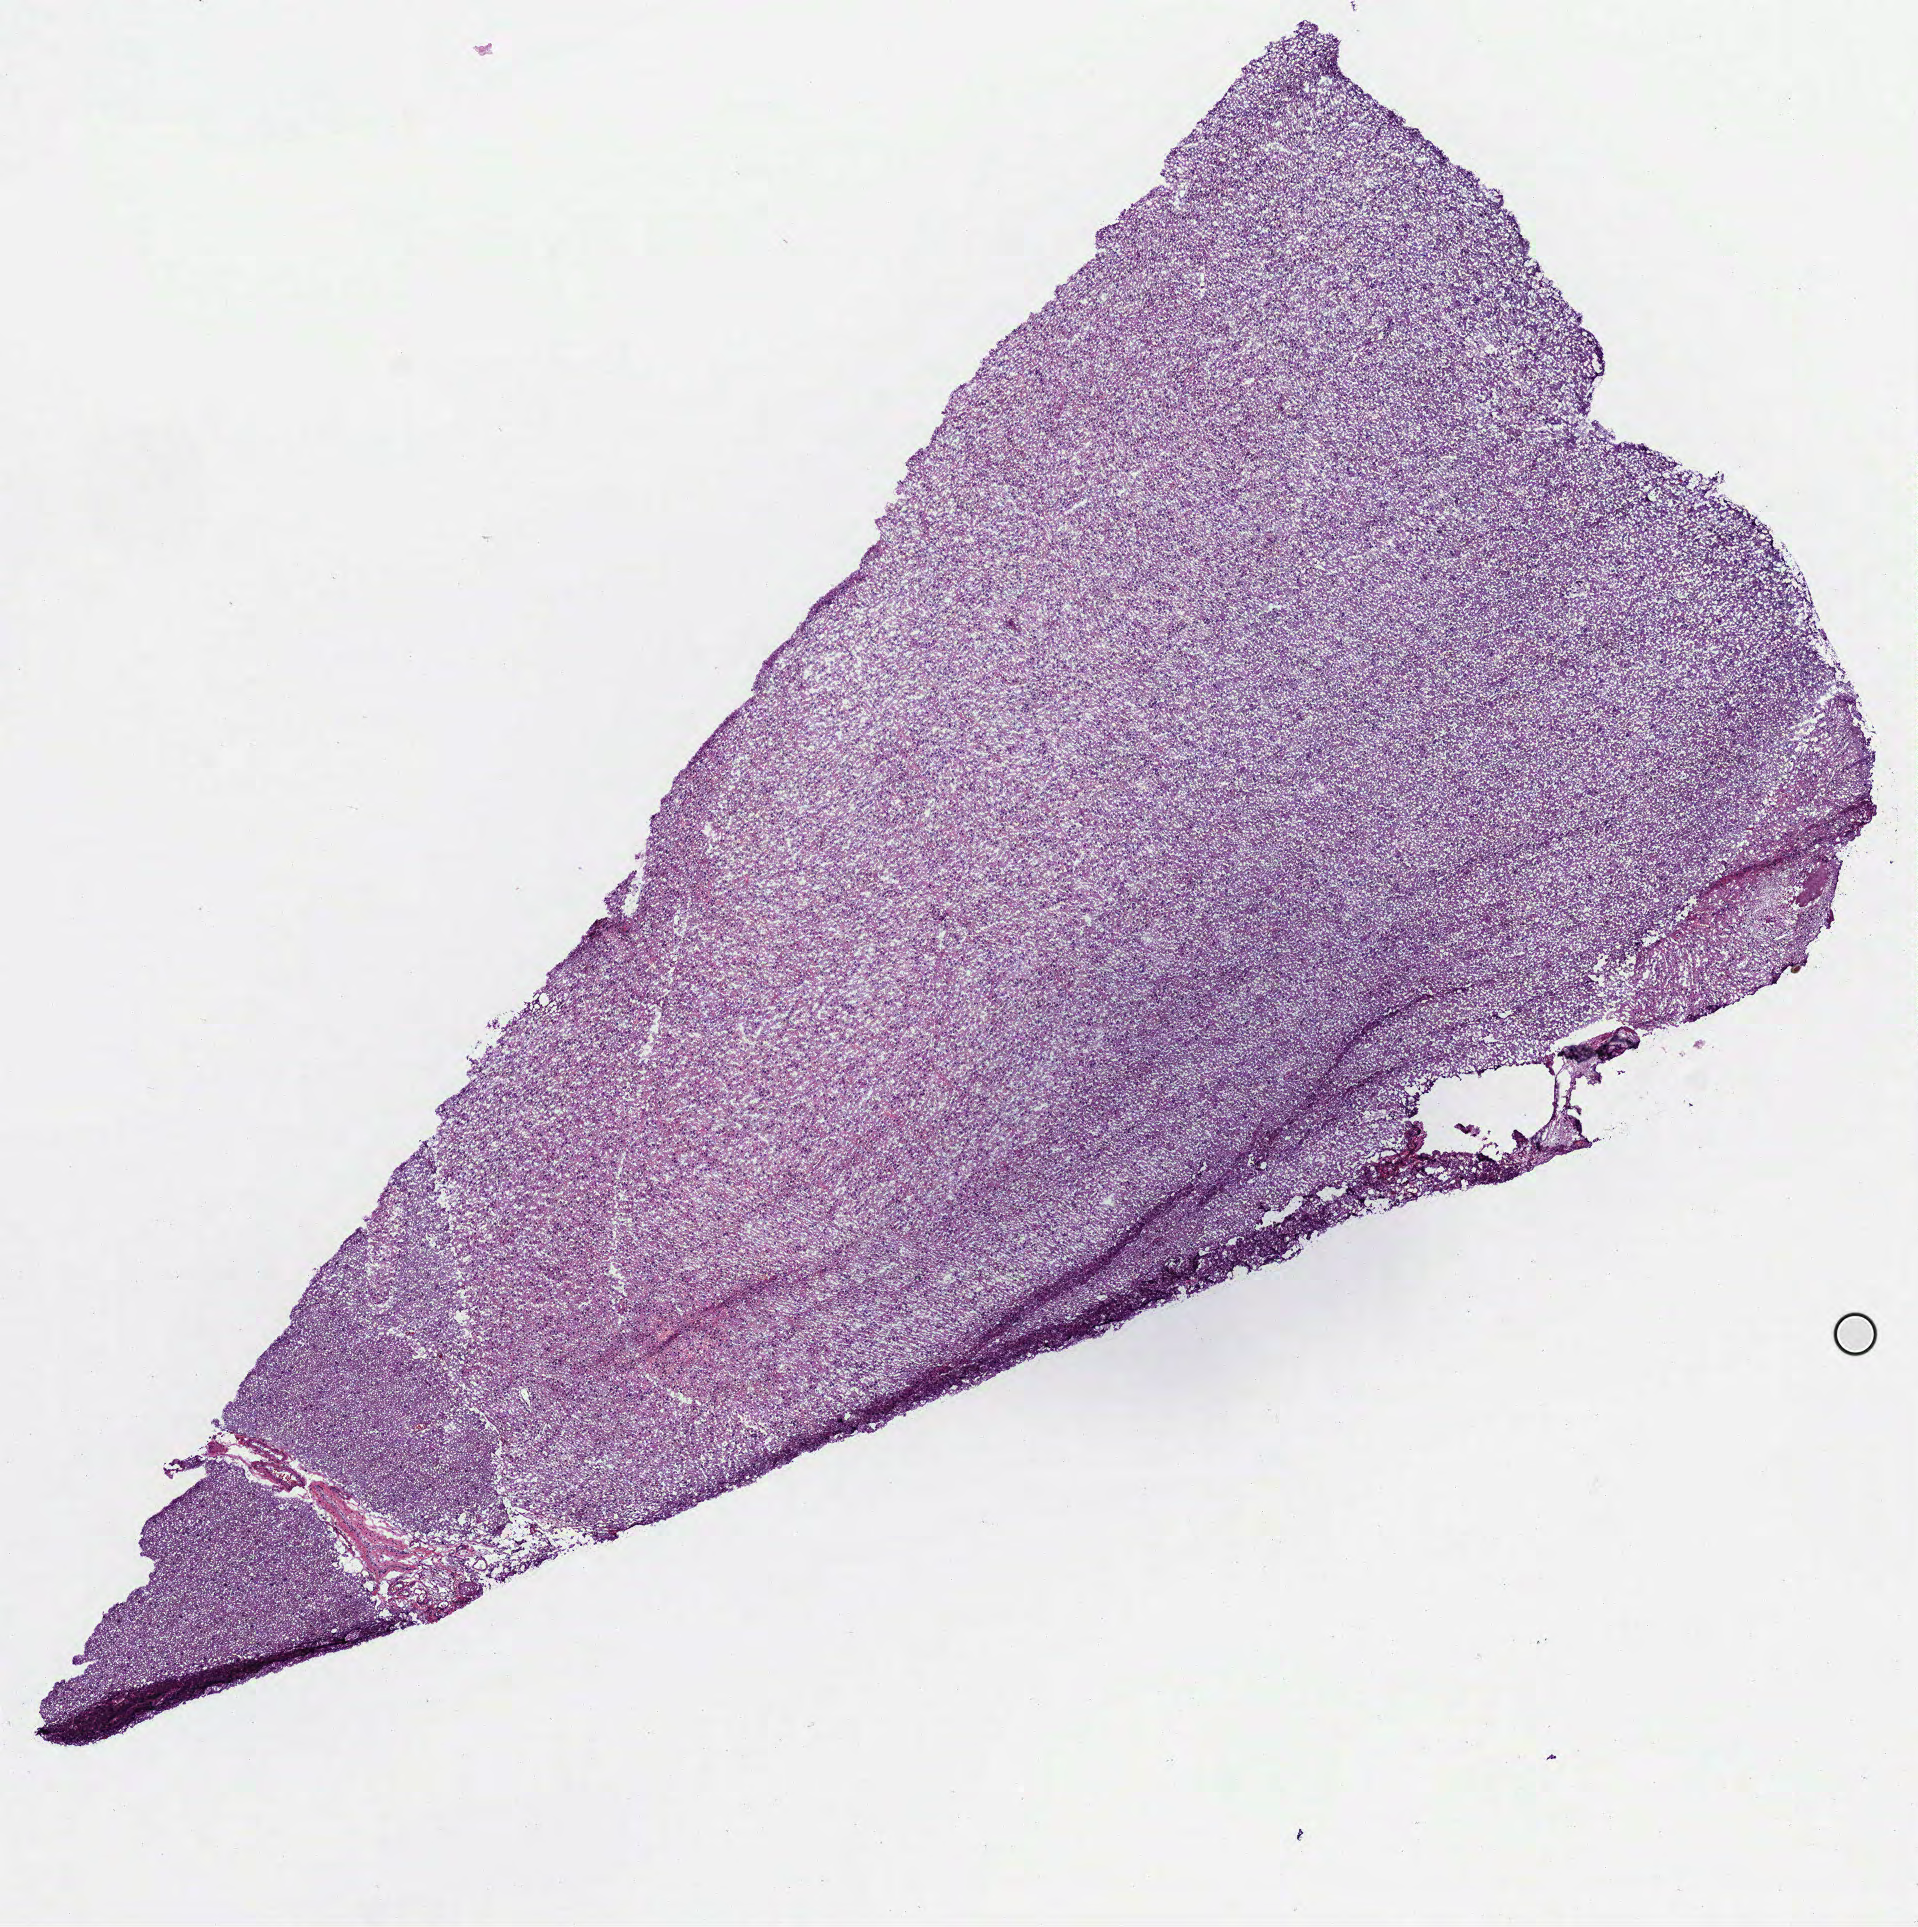
H&E-stained whole-slide image, a low-resolution overview of the entire scanned area, about 7.7 x 7.8 mm (from a 40x scan). Frozen section. Brain, primary tumour sample. Patient: female, age at initial diagnosis 20 years. Histologic grade: G2 (moderately differentiated). Pathologist review of this section (percent, as recorded): tumour cells 97%, tumour nuclei 65%, normal cells 3%, stromal cells 0%, necrosis 0%.
- histologic diagnosis: Oligodendroglioma, NOS (cerebrum)
- laterality: left